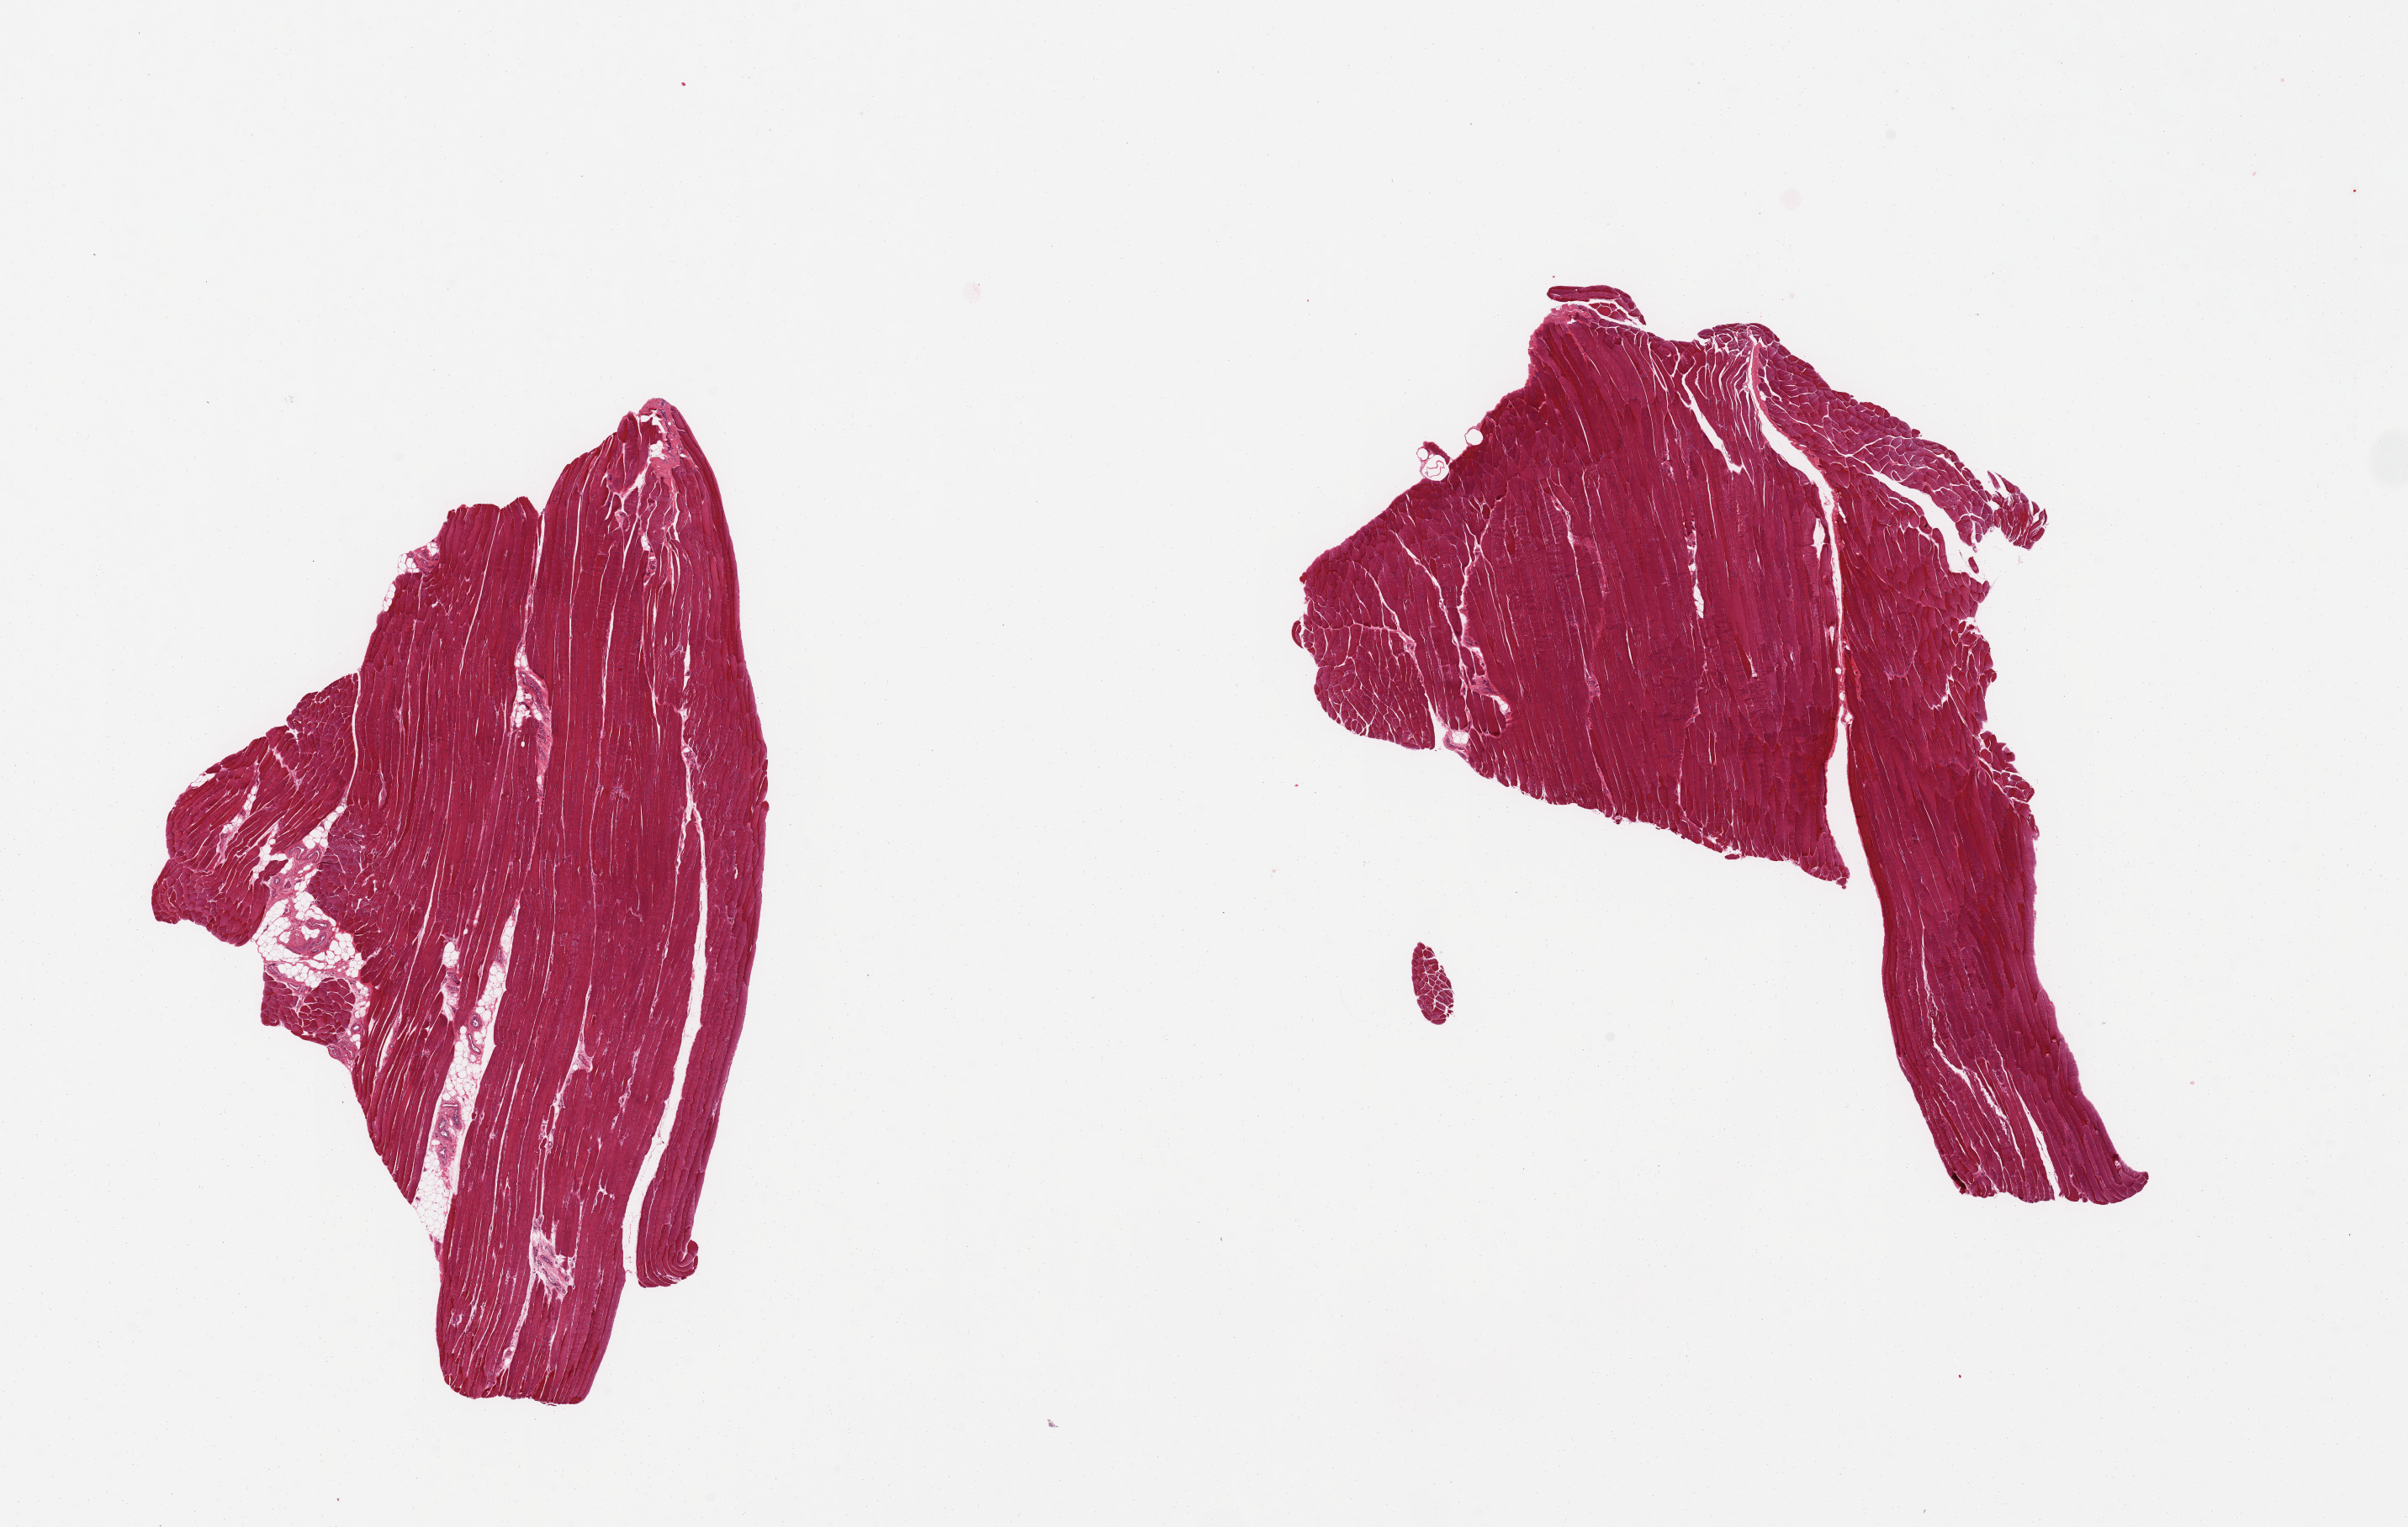
Digitized H&E-stained section, low-resolution overview of the scanned area, about 22.6 x 14.4 mm, PAXgene-fixed, paraffin-embedded tissue, sampled site (target tissue): skeletal muscle, donor tissue sample. Male donor.
Pathologist's review note for this sample: 2 pieces, minimal internal fat.